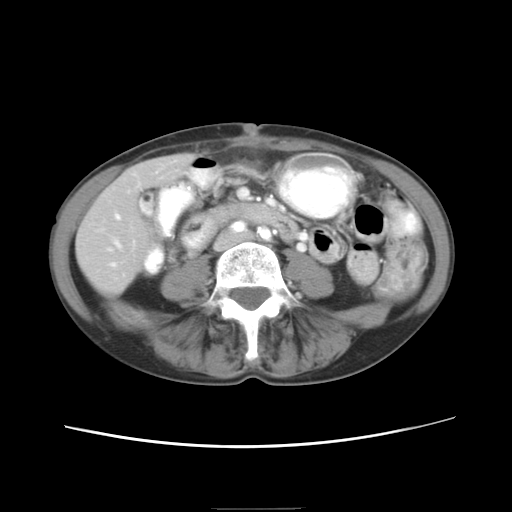
Contrast-enhanced abdominal CT, one axial slice; position 2 of 26 along the scan axis; reconstruction kernel STANDARD; 120 kVp; intravenous contrast given; soft-tissue window (W 400 / L 40 HU); 512 × 512 image matrix, field of view 340 × 340 mm. Female patient, age 65 years. Case-level facts recorded for this patient, not image findings: diagnosis: colorectal cancer liver metastases, imaged before liver resection.
Annotated regions visible in this slice (expert manual segmentation):
- hepatic veins: bounding box [x1, y1, x2, y2] px = [111, 214, 134, 266]
- liver: [78, 155, 190, 293]
- planned liver remnant (the part of the liver to remain after resection): [78, 155, 190, 293]
- portal vein (with intrahepatic branches): [108, 241, 118, 250]